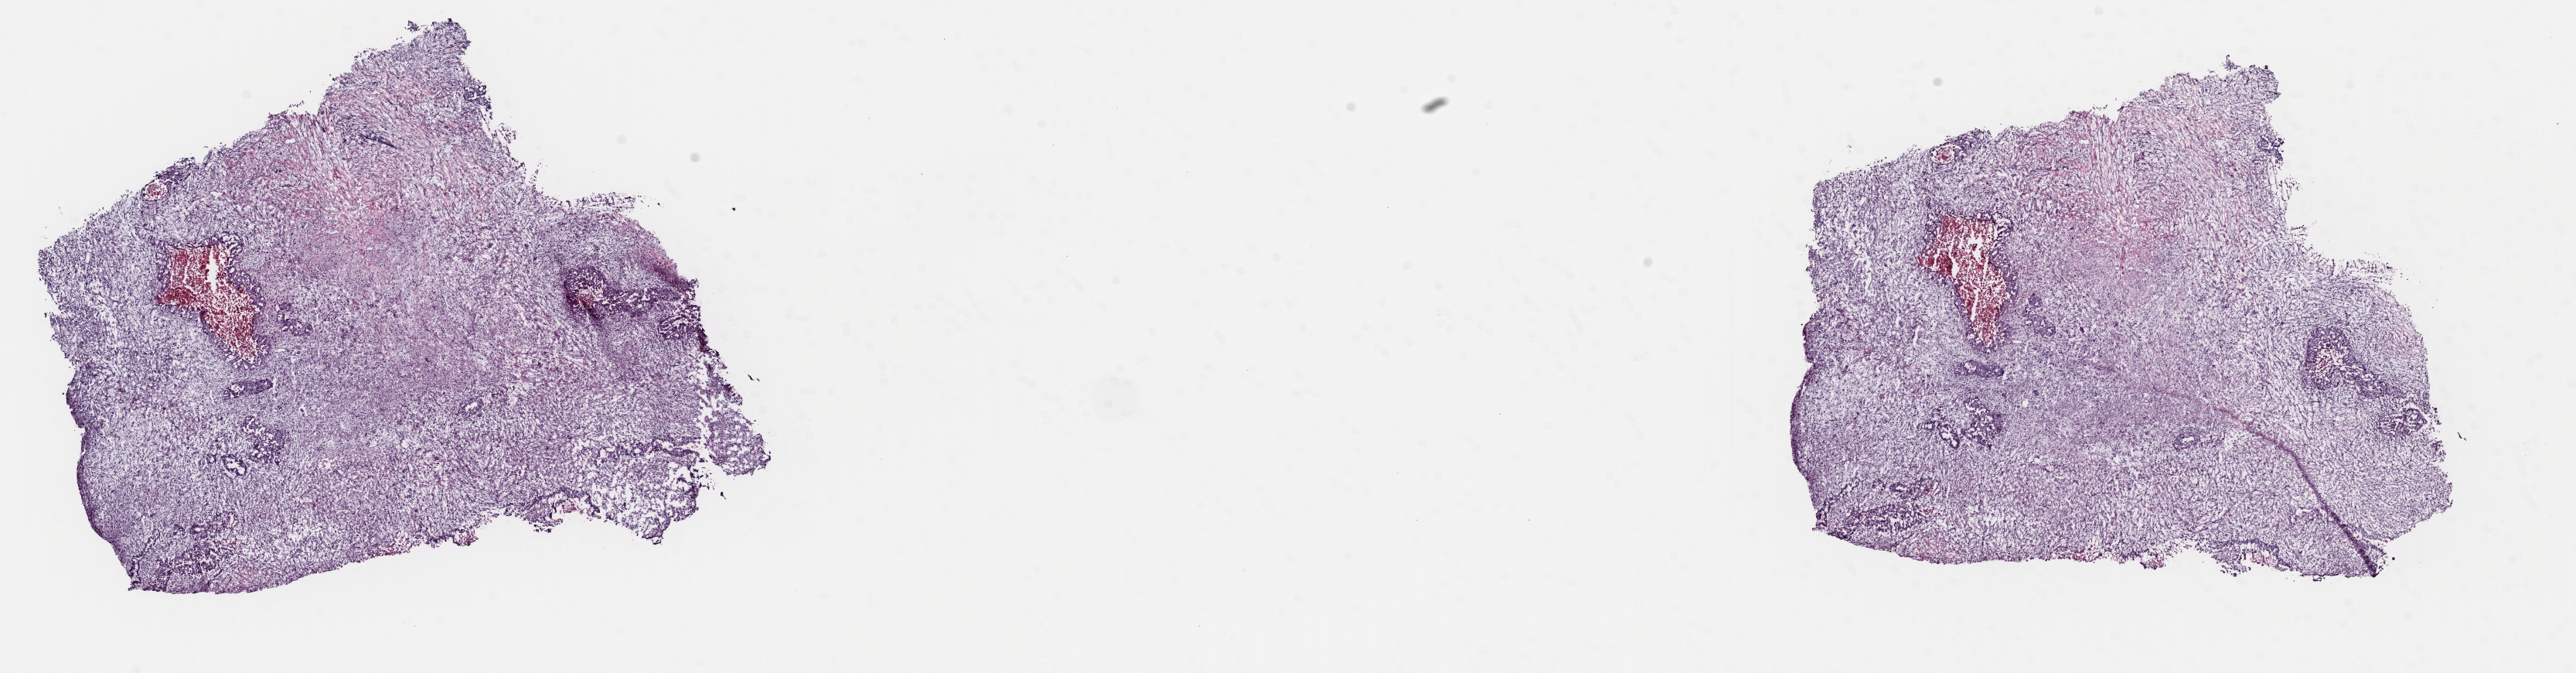
Digitized H&E-stained tissue section (whole slide) — a low-resolution overview of the entire scanned area, about 26.3 x 6.9 mm (slide scanned at 40x); frozen section; primary tumour sample from the uterus. Female patient. Pathologist review of this section (percent, as recorded): tumour cells 90%, tumour nuclei 90%, normal cells 0%, stromal cells 10%, necrosis 0%. Inflammatory infiltration, as recorded: lymphocyte infiltration 40%, monocyte infiltration 20%, neutrophil infiltration 20%.
FIGO stage: IIIC2. Pathologic diagnosis: Mullerian mixed tumor.